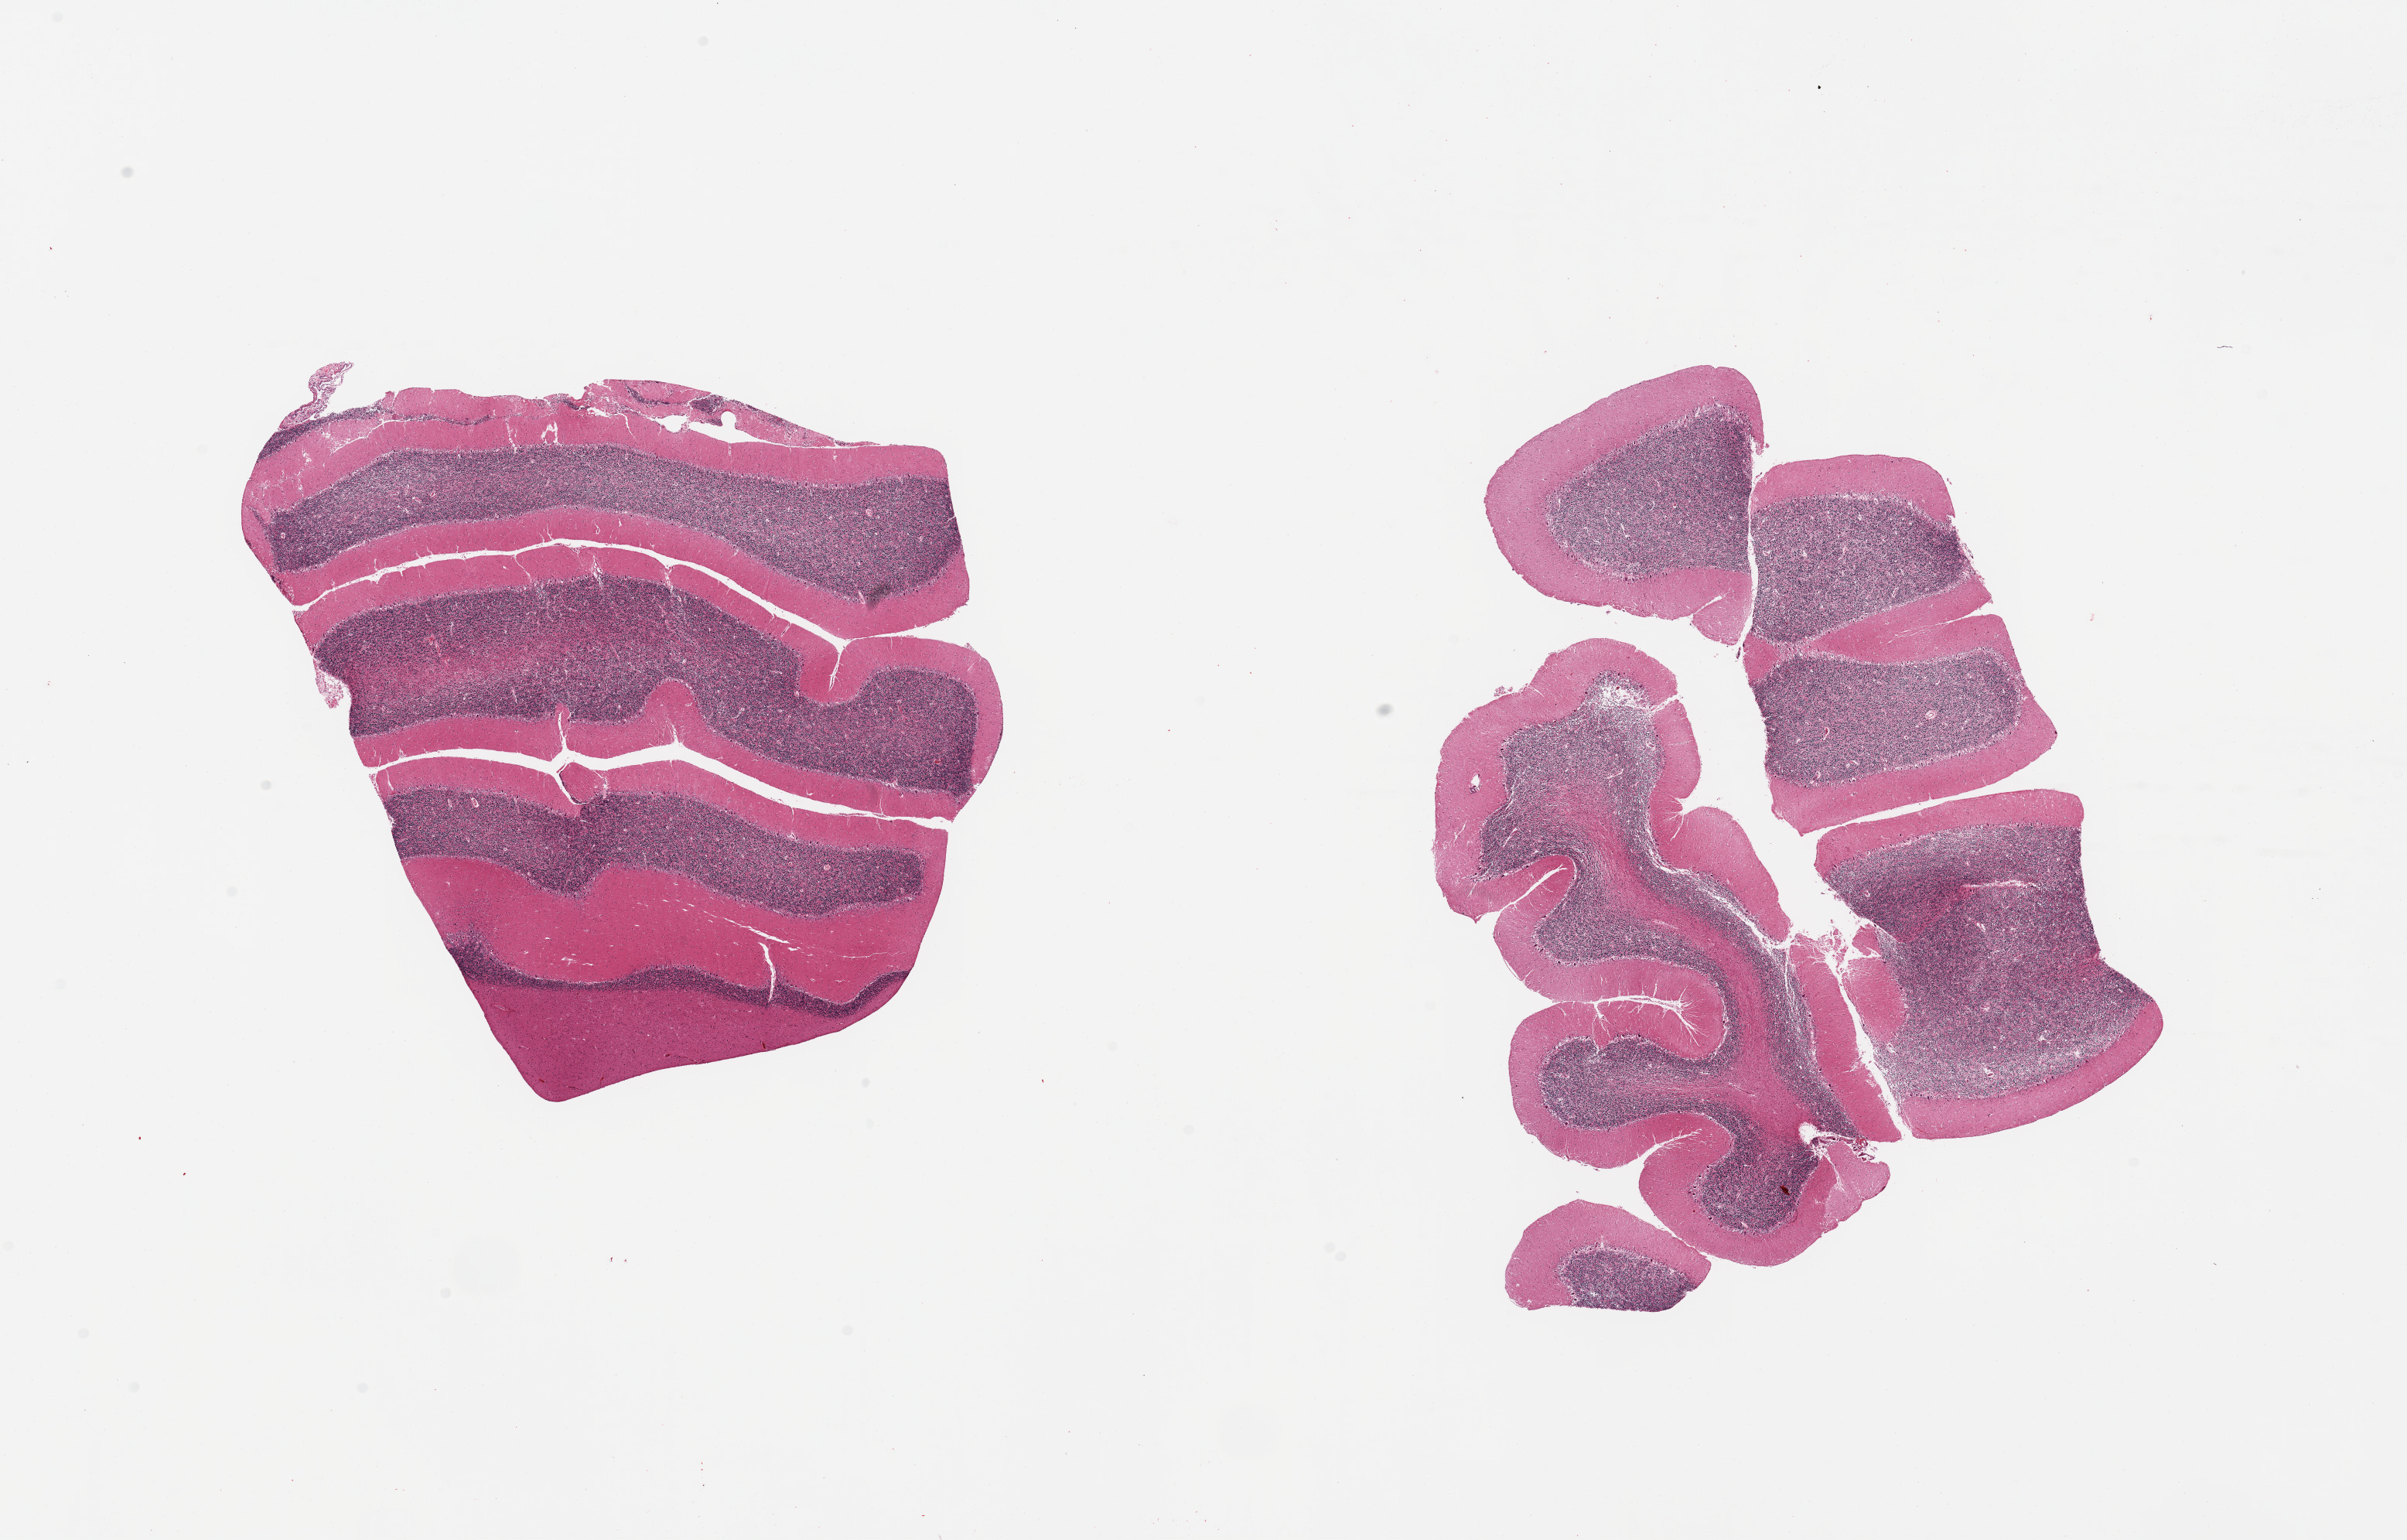
Hematoxylin and eosin (H&E) whole-slide image — shown as a low-resolution overview of the whole scanned area (about 24.6 x 15.7 mm). PAXgene-fixed paraffin-embedded (PFPE) section. Sampled site (target tissue): cerebellum. Donor tissue sample. Male donor.
Pathologist's review note for this sample: 2 pieces, no abnormalities; Purkinje cells well visualized.